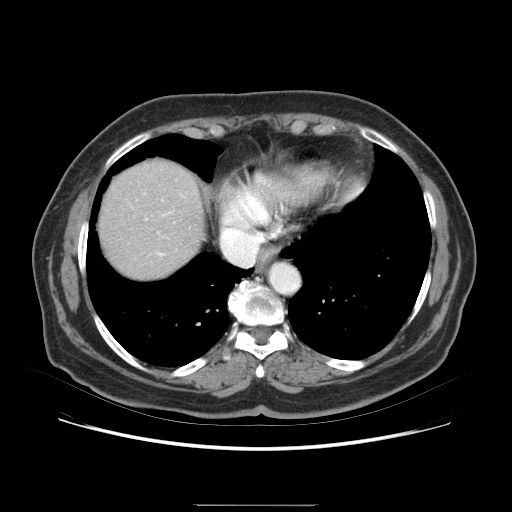
Contrast-enhanced abdominal CT (liver protocol), one axial slice; slice 72 of 79 in the series (ordered by position); 120 kVp; soft-tissue window (W 400 / L 40 HU); 2.5 mm slice thickness; 512 × 512 image matrix, field of view 380 × 380 mm. From the clinical record (not read from this slice): diagnosis: hepatocellular carcinoma (patient treated with transarterial chemoembolisation; whether this scan precedes or follows treatment is not stated here); TNM stage (as recorded): Stage-I; Child-Pugh class: A.
Outlined on this slice (semi-automatically segmented with operator editing):
- liver parenchyma outside the tumour (the mass and vessels are separate outlines, so this box may not span the whole liver): bounding box [x1, y1, x2, y2] px = [116, 170, 192, 250]